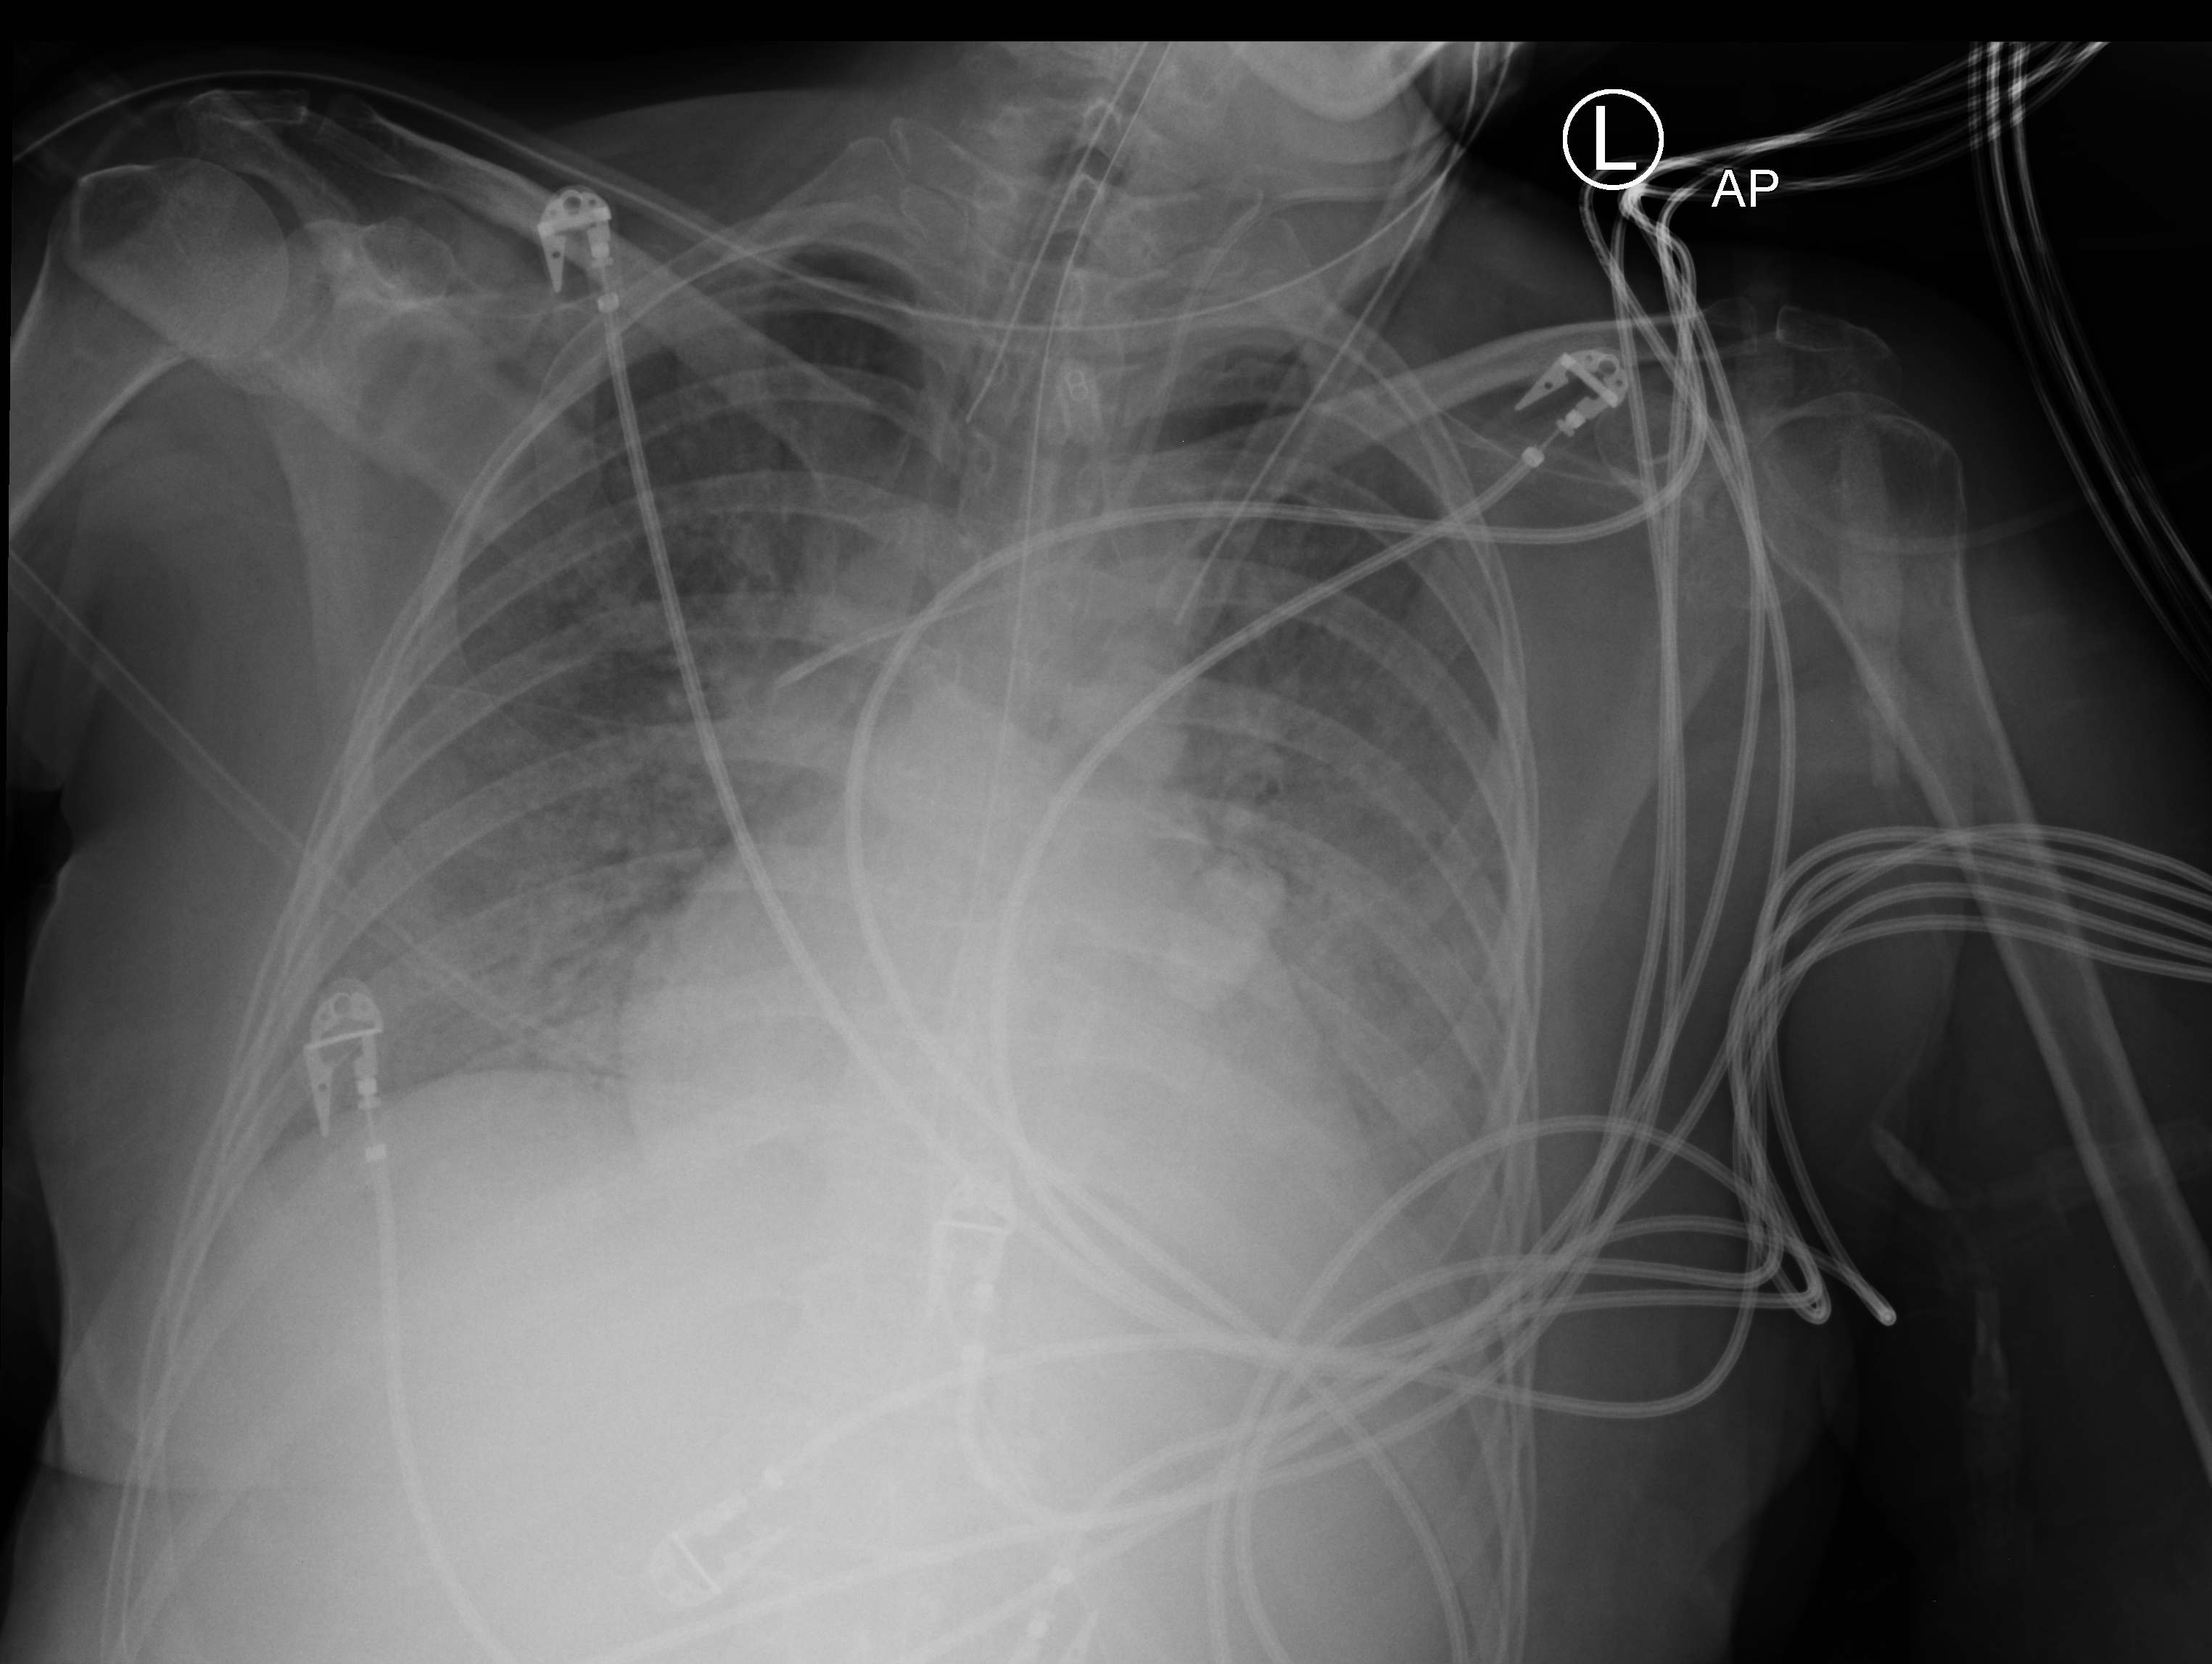
Bedside chest radiograph (computed radiography). Adult patient hospitalised with COVID-19, age 18–59 years.
Hospital-stay facts (about this admission, not read from this image; timing relative to this image not recorded):
- admitted to intensive care during this hospital stay: yes
- mechanically ventilated during this hospital stay: yes
- length of hospital stay: 10 days